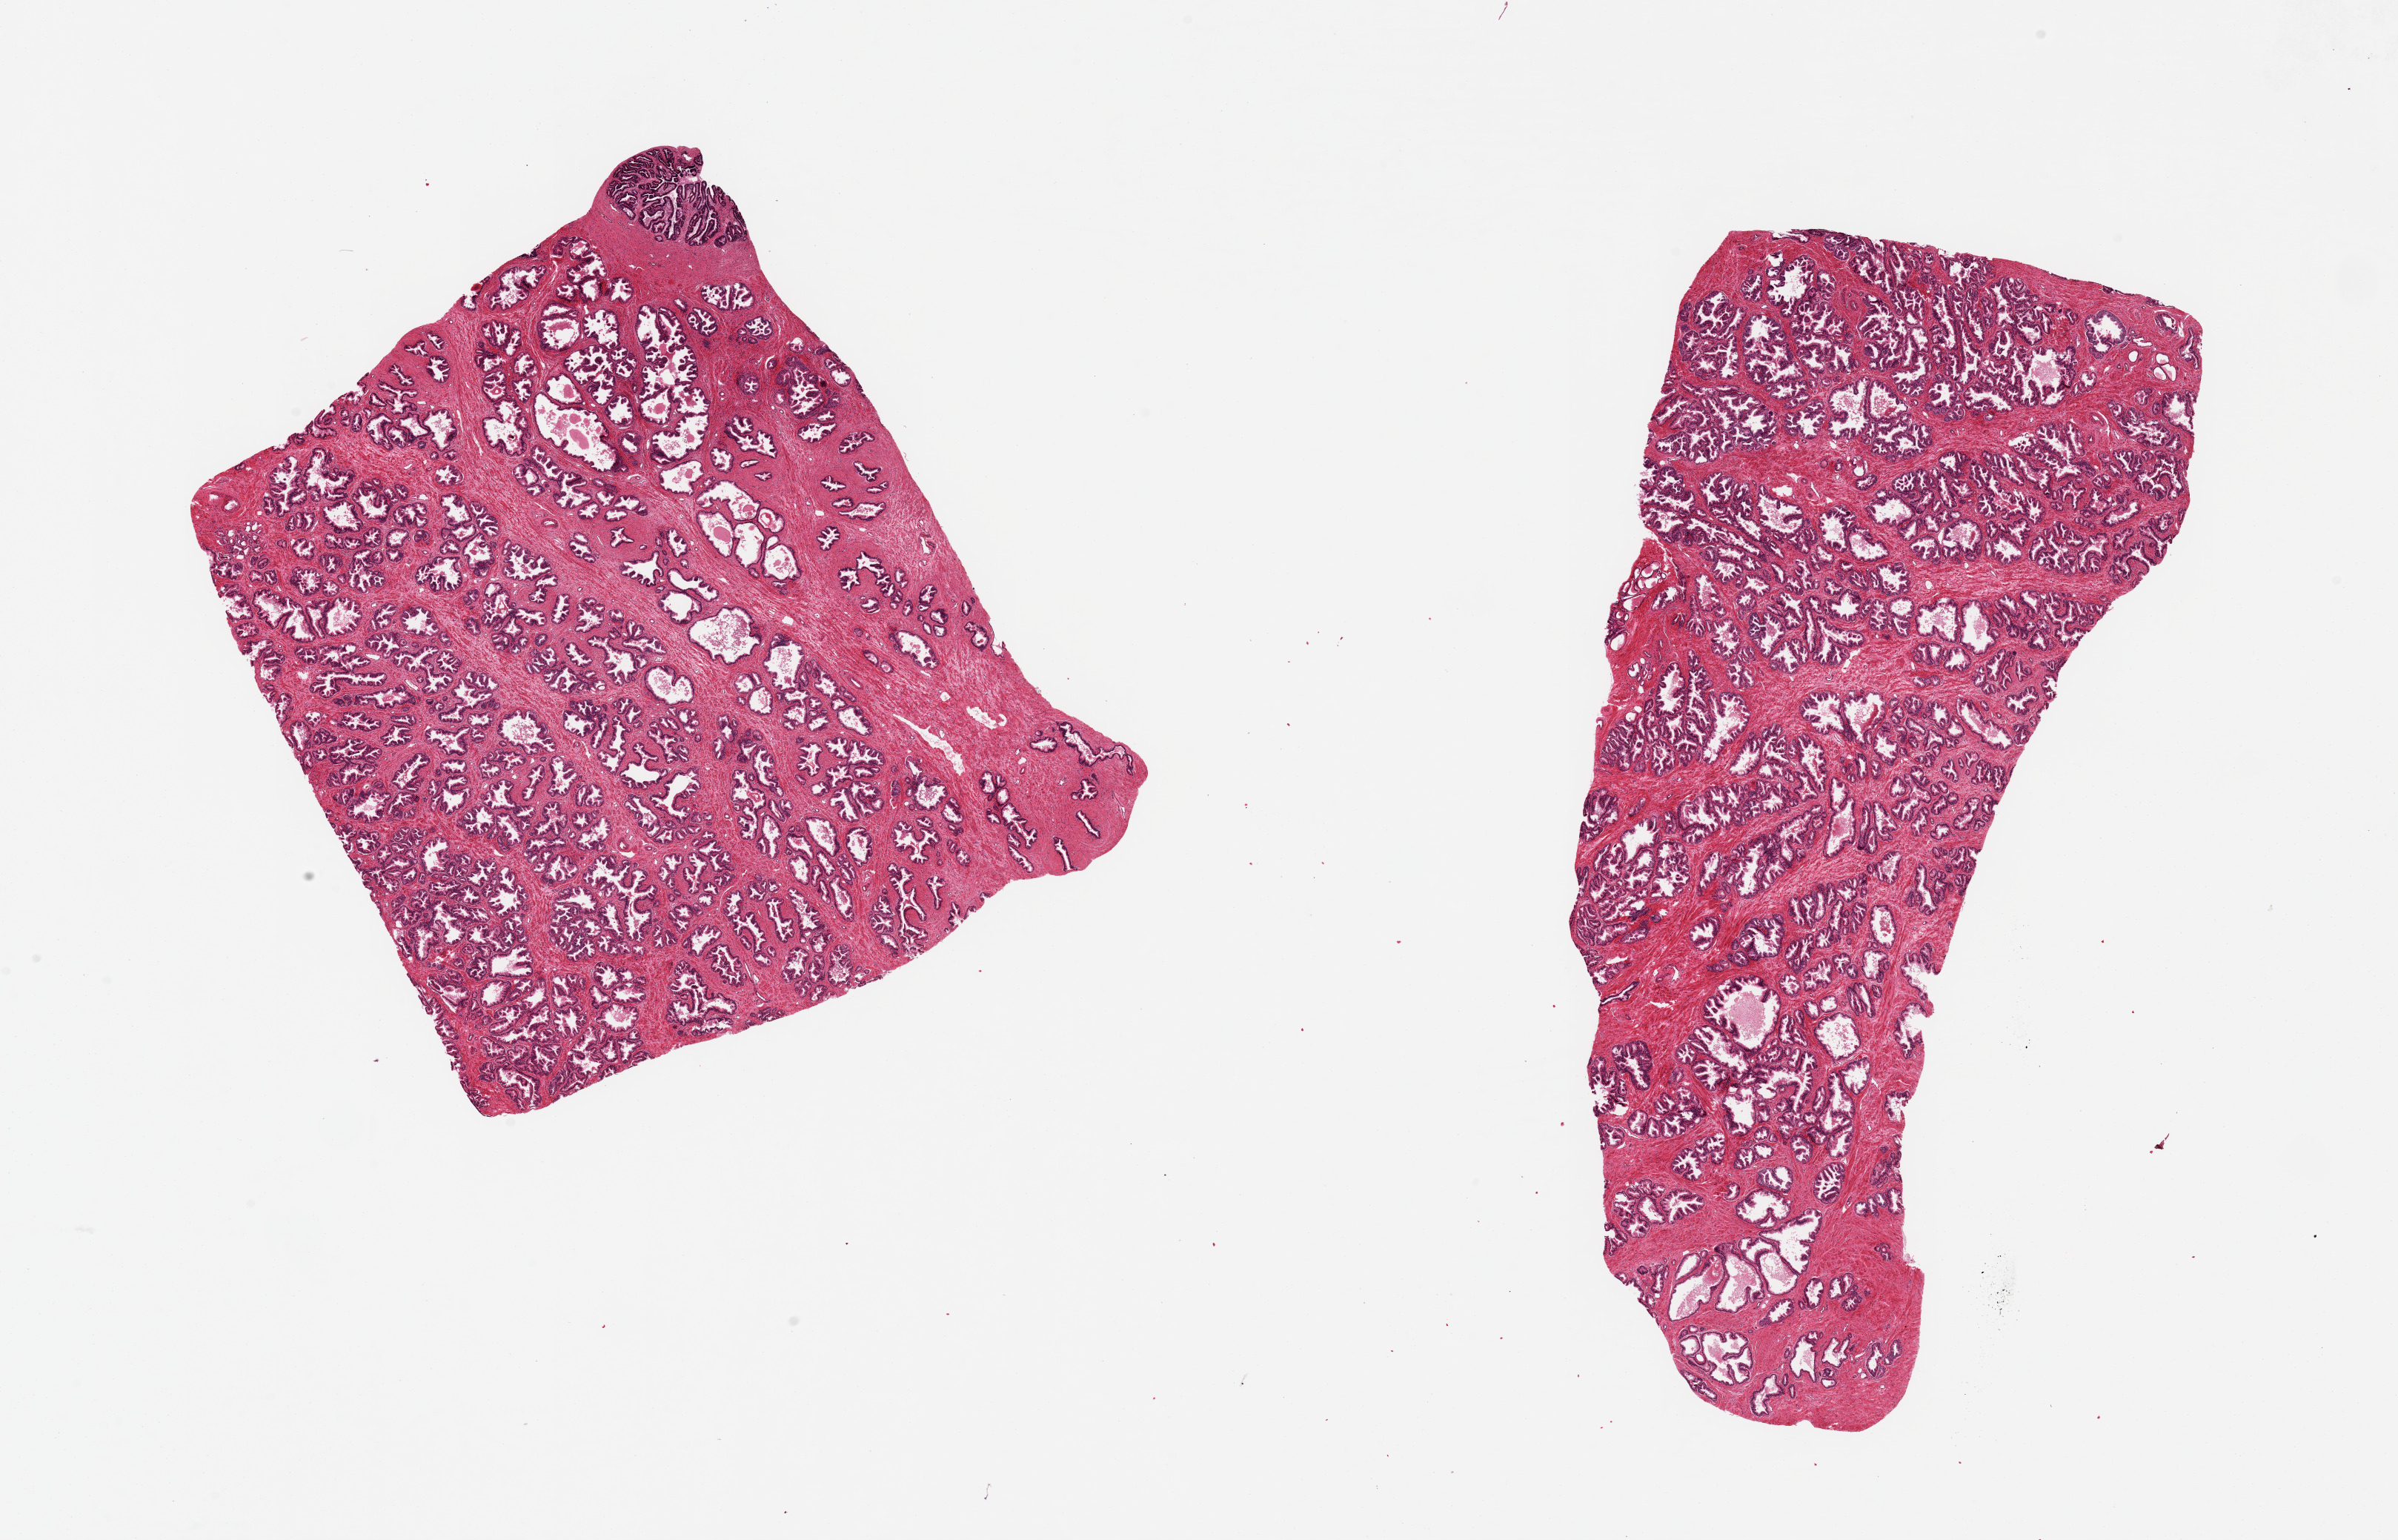
Digitized H&E-stained section, low-resolution overview of the scanned area, about 25.6 x 16.4 mm, PAXgene-fixed paraffin-embedded (PFPE) section, section of prostate (target tissue), tissue donor sample. Donor sex: male.
Reviewer comment on this tissue sample: 2 pieces ~9x7mm. Note: ~1.5mm focus of seminal vesicle in one. Glands well -preserved.